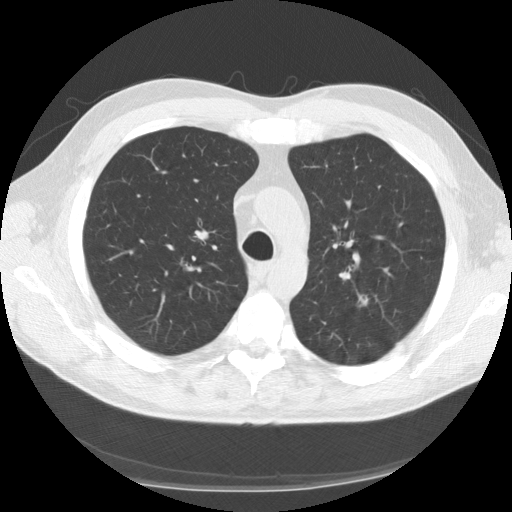
Axial slice from a low-dose chest CT screening exam, second screening round (one year after baseline), lung window (W 1500 / L -600 HU), standard (soft-tissue) reconstruction kernel (STANDARD), 120 kVp, slice 40 of 152 in the series. Male, age 57 years at enrolment. Current smoker at enrolment.
Expert-annotated lung lesion, bounding box <342,284,381,325> (left, top, right, bottom; pixels). The exam's reader record, not a measurement of the box and not confirmed to be the same lesion: non-calcified nodule or mass ≥4 mm, left upper lobe, 12 × 7 mm, spiculated (stellate) margins, mixed attenuation, pre-existing on the prior screen: no. Official screen result: positive, other. Later outcome: lung cancer diagnosed 419 days after this screen (after the third annual screen) — adenosquamous carcinoma, left upper lobe, poorly differentiated (G3), stage IA (AJCC 6th edition), 15 mm at pathology.